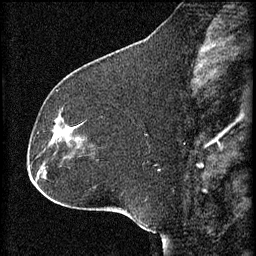
Breast MRI (dynamic contrast-enhanced), one sagittal slice; slice 24 of 60 in the series (ordered by position); 3 images stored at this slice position (order not interpretable as contrast timing); 1.5 T; TE 4.2 ms, TR 8.2 ms; 256 × 256 image matrix, field of view 180 × 180 mm. Patient: female, 32 years.
Structures marked on this image (semi-automatically segmented with operator editing):
- analysis volume of interest (the breast-tissue region the enhancement analysis was run in; not a lesion): bounding box (x1, y1, x2, y2) in pixels: (47, 114, 84, 157)
- tumour enhancement mask (voxels above the 70 % enhancement threshold inside the analysis volume of interest): (53, 126, 70, 143)